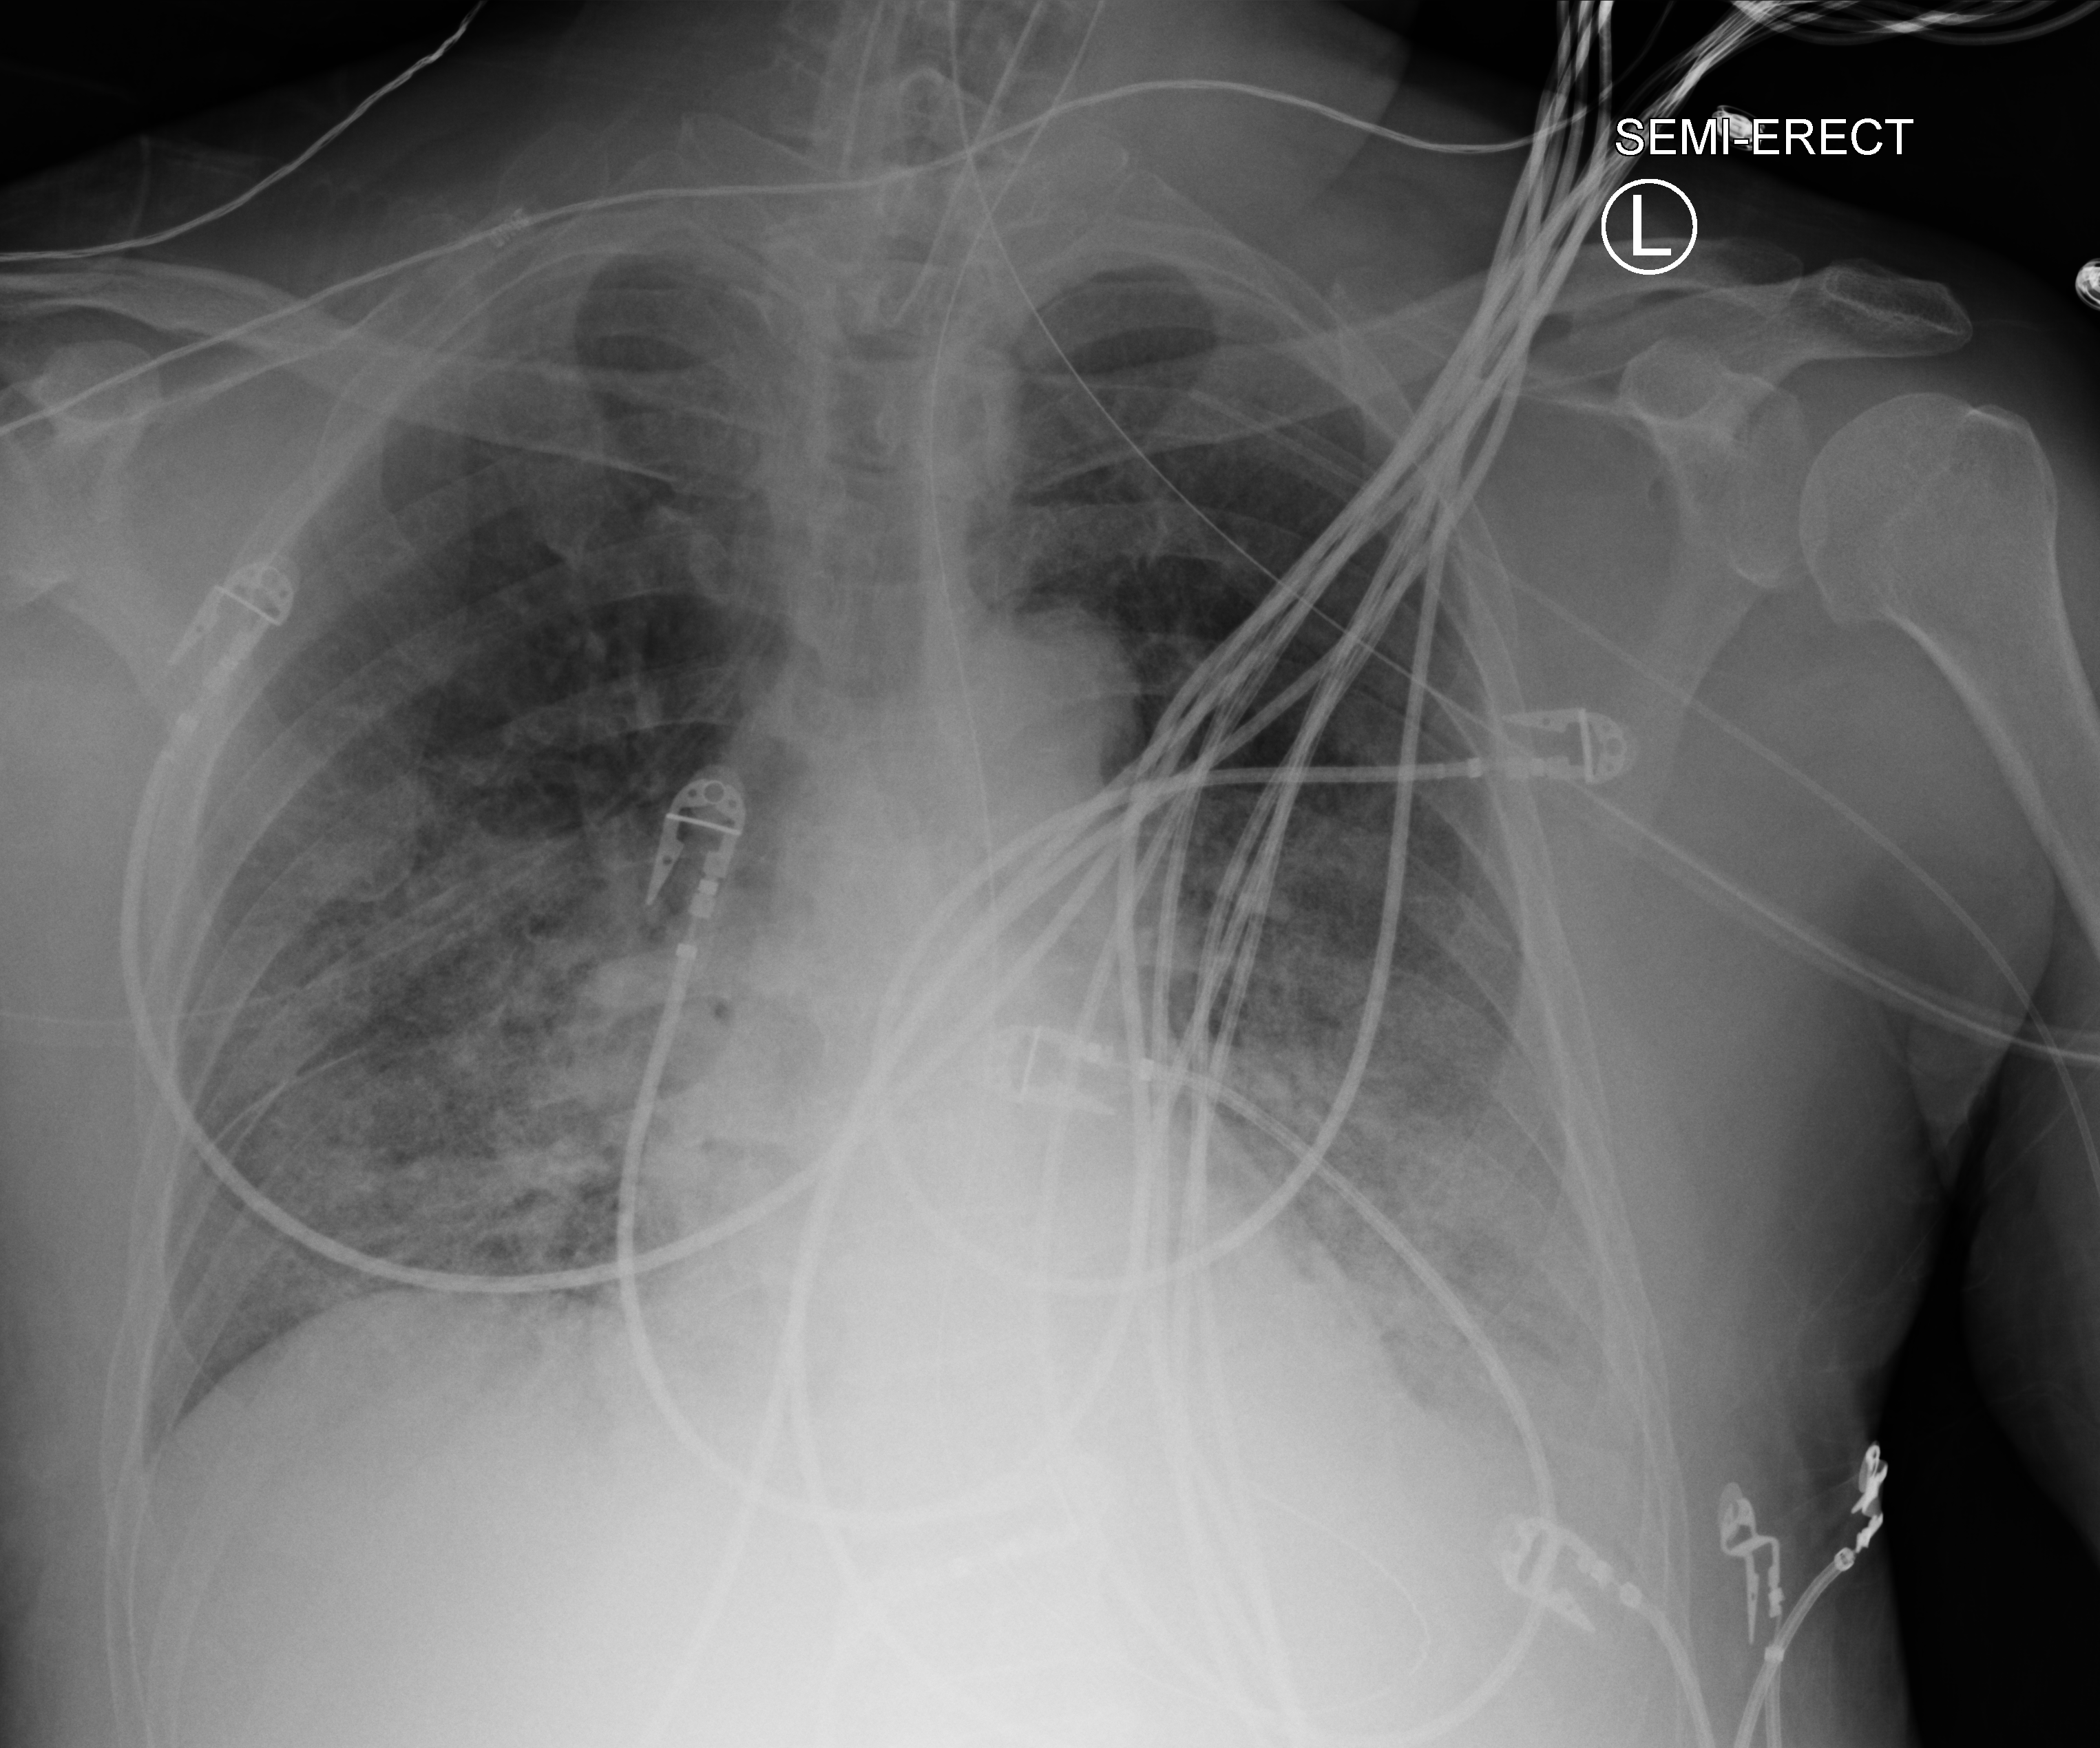
Chest X-ray (portable), anteroposterior (AP) projection. Patient hospitalised with COVID-19; male, aged 60–74 years.
Admission-level facts for this patient (not findings on this image; timing relative to this image not recorded):
- mechanically ventilated during this hospital stay: yes
- chronic kidney disease (admission record): no
- length of hospital stay: 14 days